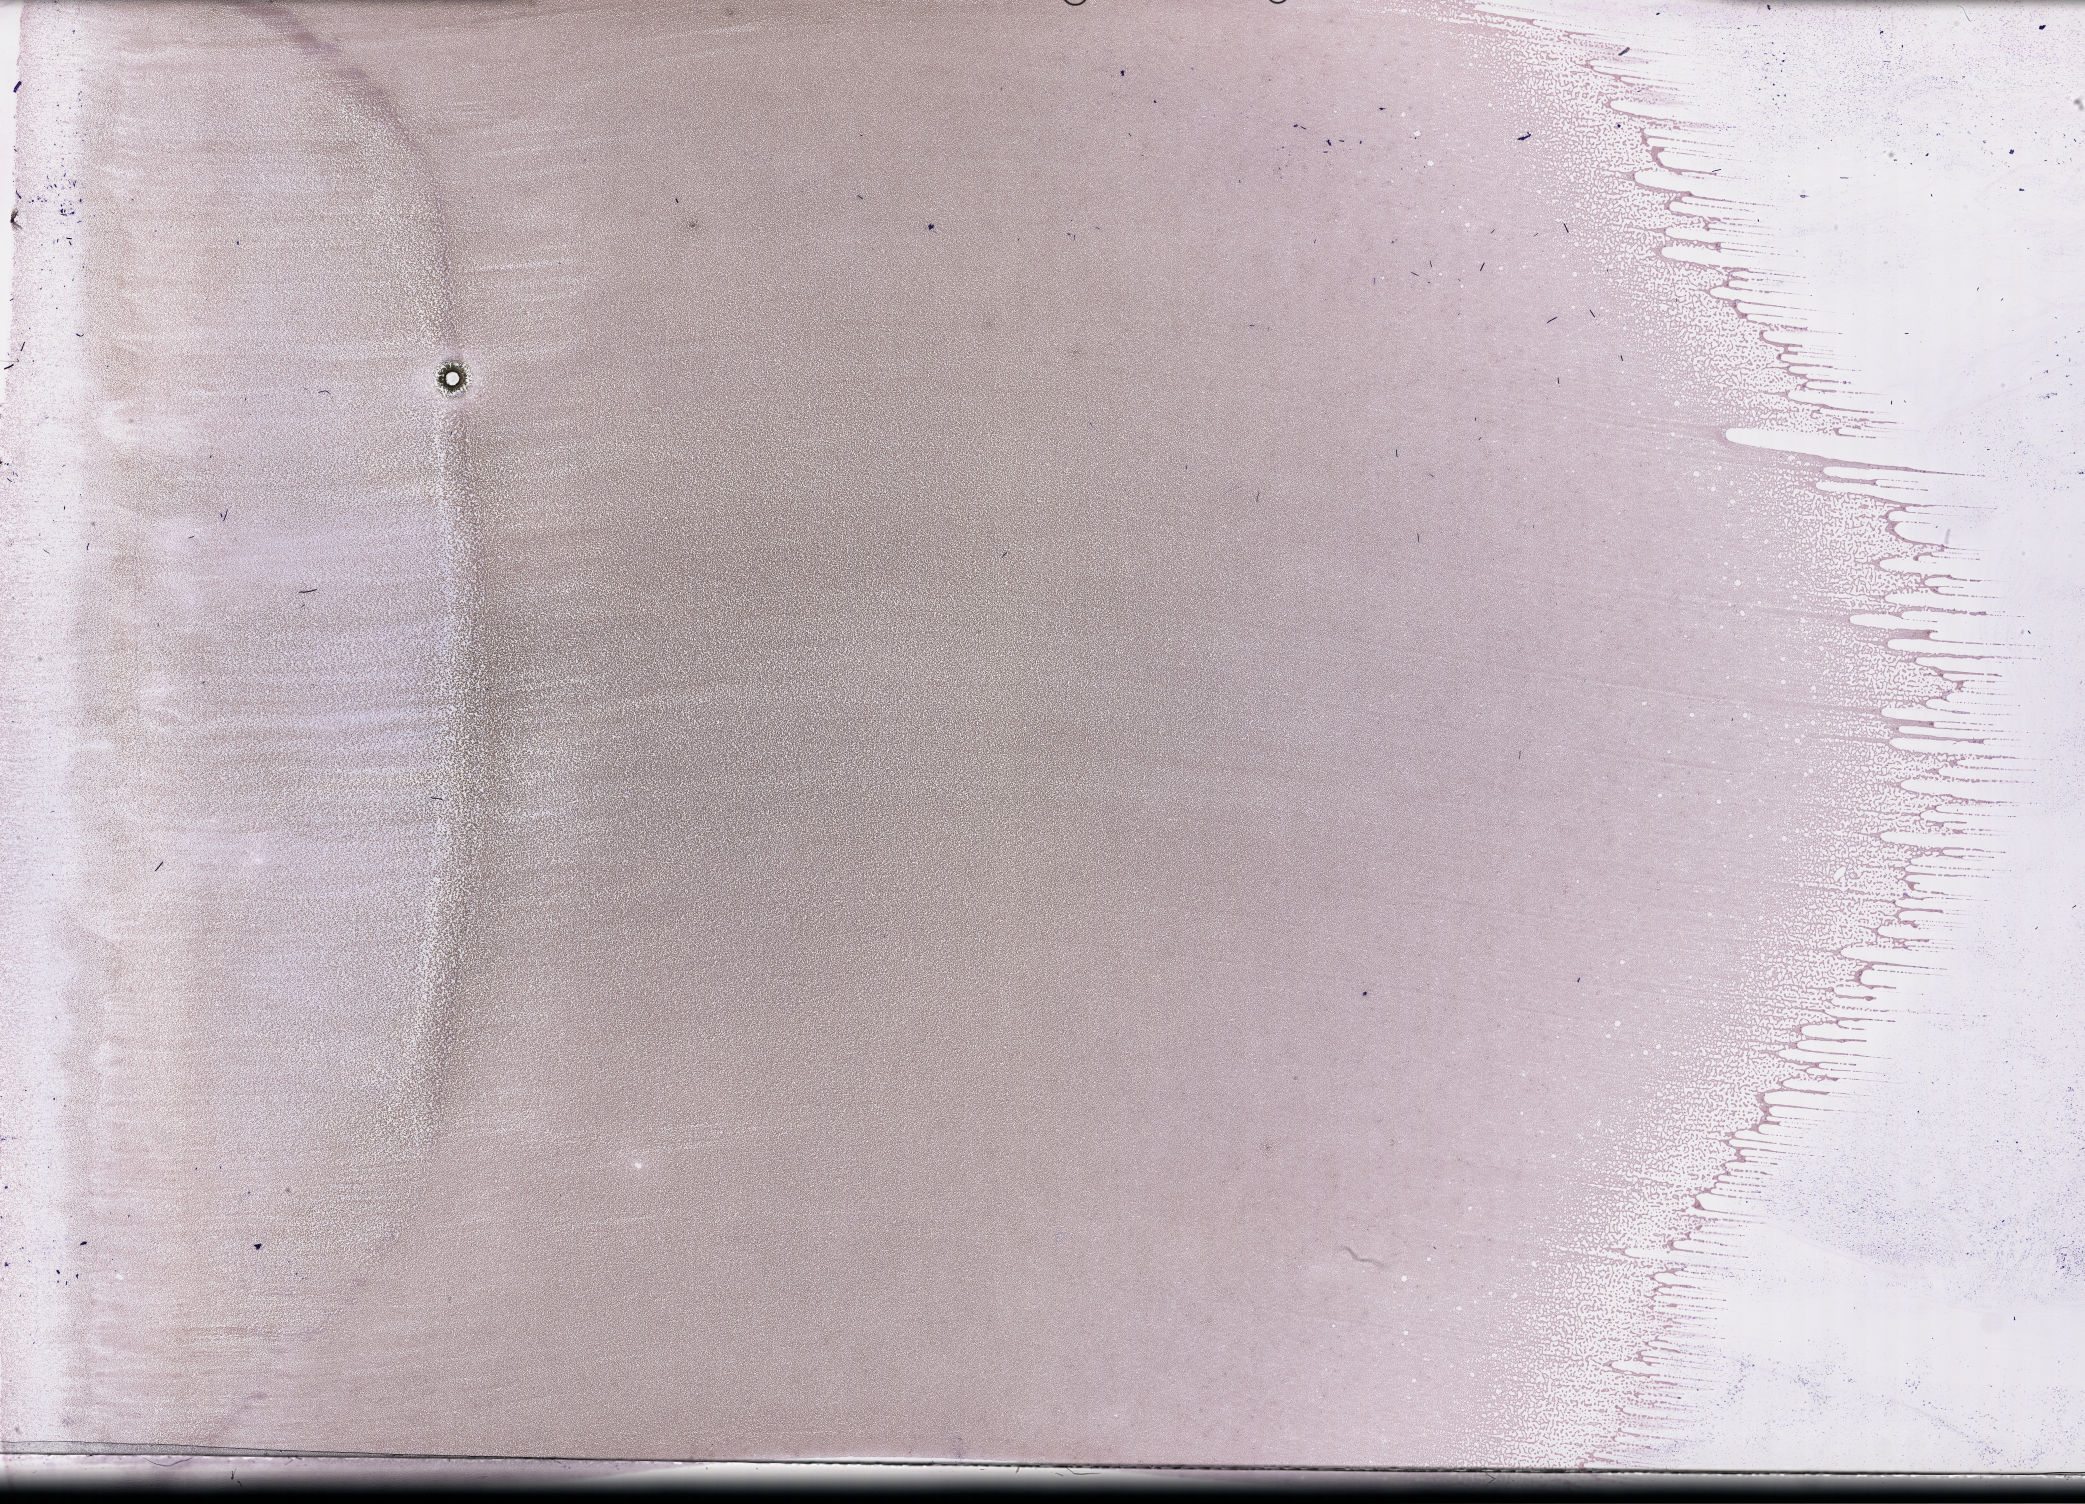
Wright-Giemsa-stained whole blood smear, whole-slide image, shown as a low-resolution overview of the whole scanned area (about 33.7 x 24.3 mm). Patient: female.
From a patient with: Plasma Cell Myeloma.